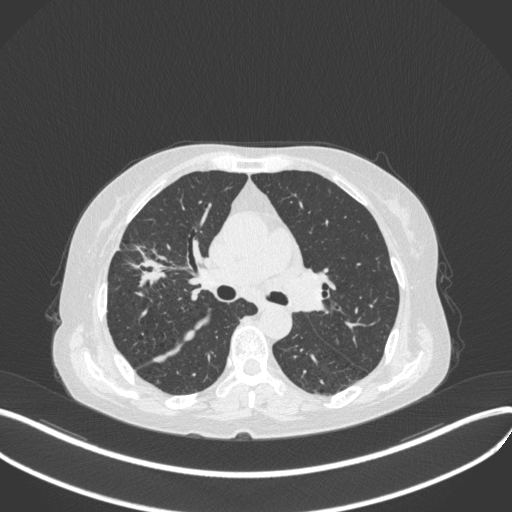
Chest CT, one axial slice. Position 243 of 429 along the scan axis. Reconstruction kernel B31f. Lung window (W 1500 / L -600 HU). 512 × 512 image matrix, field of view 400 × 400 mm. Patient: female, 69 years. Case-level facts recorded for this patient, not image findings: clinical TNM (as recorded): T1b N3 M0.
Structures marked on this image (rectangle marked by the reading radiologist):
- lung tumour (recorded histology: small cell carcinoma): bounding box <120,246,175,293> (left, top, right, bottom; pixels)